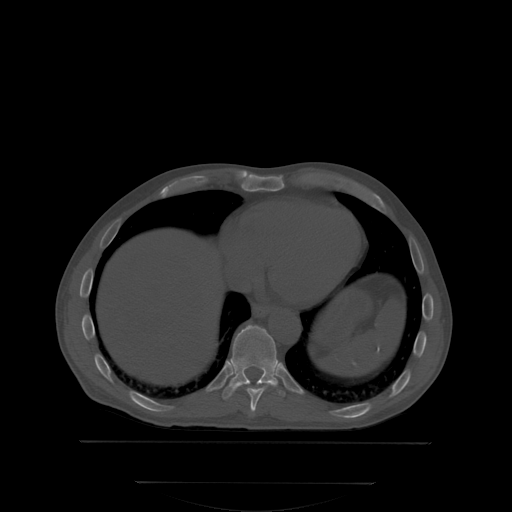
CT including the spine, one axial slice; position 198 of 350 along the scan axis; bone window (W 1800 / L 400 HU); 2.5 mm slice thickness; 512 × 512 image matrix, field of view 500 × 500 mm. Male patient, age 58 years. From the clinical record (not read from this slice): primary cancer: prostate.
Outlined on this slice (semi-automatic segmentation, software-assisted and operator-edited):
- T10 vertebra: box from (x=223, y=325) to (x=284, y=398) px
- T9 vertebra: (x=239, y=383)–(x=275, y=413)